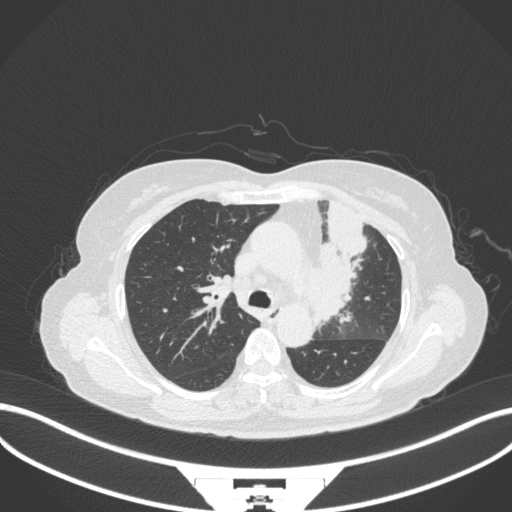
Chest CT, one axial slice; slice 226 of 382 in the series (ordered by position); 120 kVp; lung window (W 1500 / L -600 HU); 1 mm slice thickness; 512 × 512 image matrix, field of view 400 × 400 mm. Female patient, age 64 years. From the clinical record (not read from this slice): clinical TNM (as recorded): T2a N2 M0.
Annotated regions visible in this slice (rectangle marked by the reading radiologist):
- lung tumour (recorded histology: adenocarcinoma): bounding box <298,200,372,322> (left, top, right, bottom; pixels)